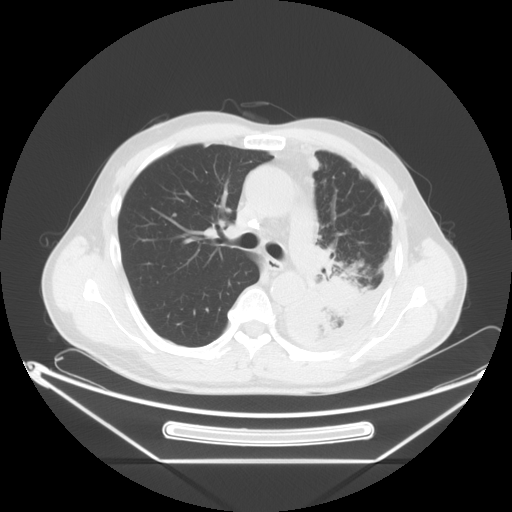
Chest CT, one axial slice. Position 40 of 63 along the scan axis. Lung window (W 1500 / L -600 HU). 512 × 512 image matrix, field of view 442 × 442 mm. Patient: male, 60 years. From the clinical record (not read from this slice): clinical TNM (as recorded): T4 N1 M1.
Annotated regions visible in this slice (bounding box drawn by a radiologist):
- lung tumour (recorded histology: adenocarcinoma): bounding box (x1, y1, x2, y2) in pixels: (303, 263, 367, 334)